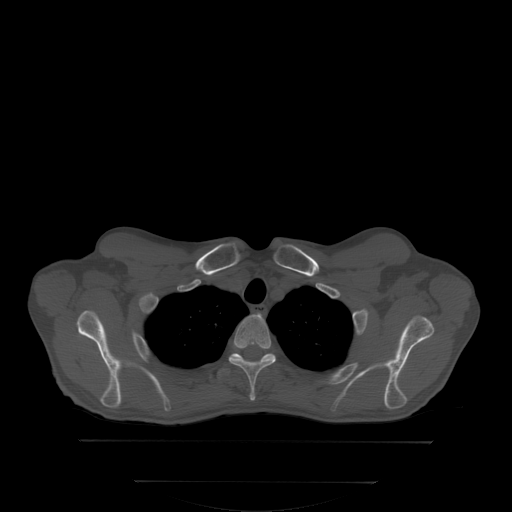
CT including the spine, one axial slice. Bone window (W 1800 / L 400 HU). 2.5 mm slice thickness. 512 × 512 image matrix, field of view 500 × 500 mm. Male patient, age 58 years. From the clinical record (not read from this slice): primary cancer: prostate.
Annotated regions visible in this slice (semi-automatic segmentation, software-assisted and operator-edited):
- T2 vertebra: bounding box [x1, y1, x2, y2] px = [232, 315, 277, 401]
- T3 vertebra: [229, 353, 272, 363]